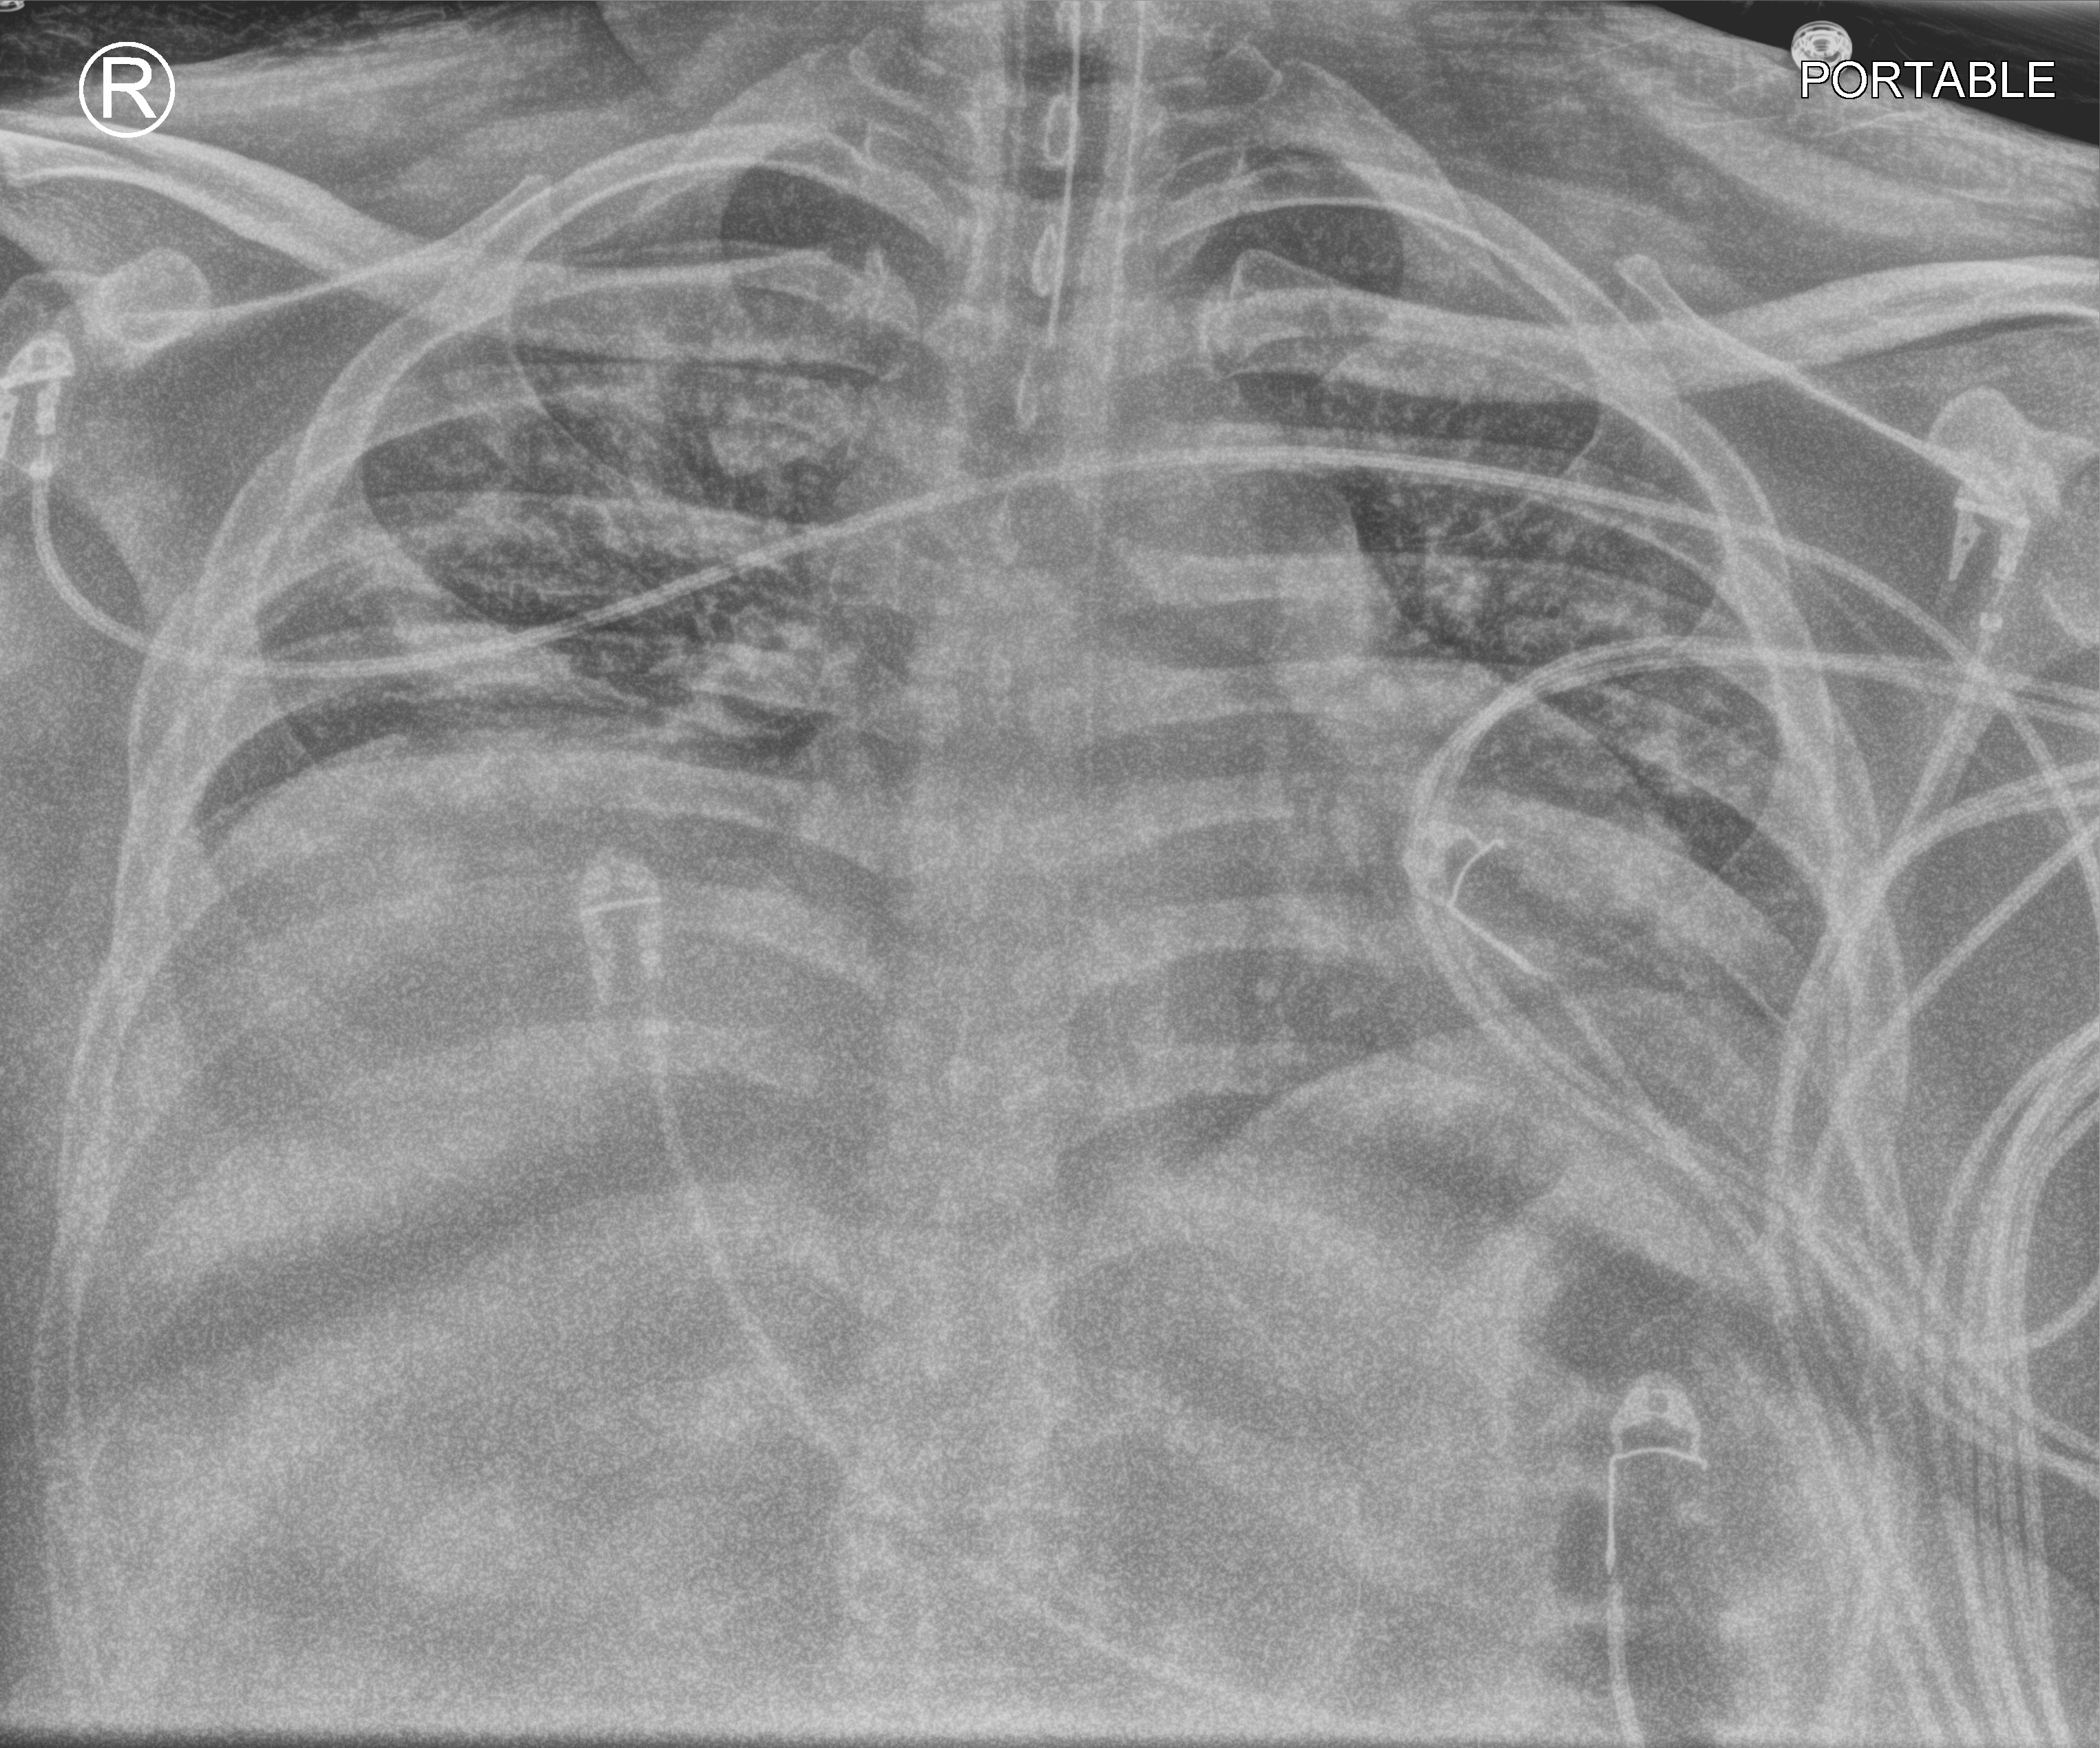
Portable chest radiograph; anteroposterior (AP) projection. Male patient hospitalised with COVID-19, age 18–59 years.
Admission-level facts for this patient (not findings on this image; timing relative to this image not recorded): length of hospital stay: 69 days.